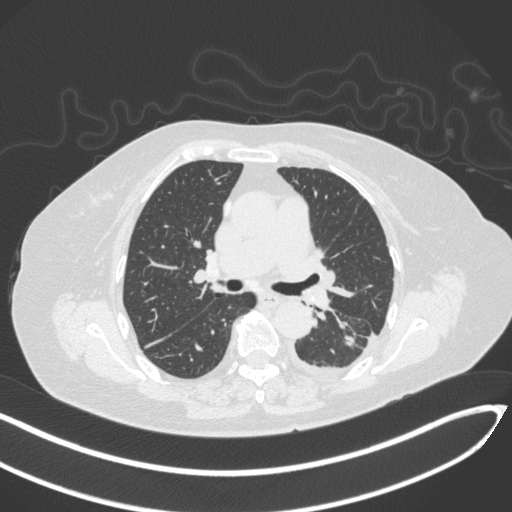
Chest CT, one axial slice; position 189 of 270 along the scan axis; 120 kVp; lung window (W 1500 / L -600 HU); 1 mm slice thickness; 512 × 512 image matrix, field of view 400 × 400 mm. Female patient, age 76 years. Case-level facts recorded for this patient, not image findings: clinical TNM (as recorded): T1c N0 M0.
Outlined on this slice (bounding box drawn by a radiologist):
- lung tumour (recorded histology: adenocarcinoma): box from (x=340, y=334) to (x=358, y=349) px